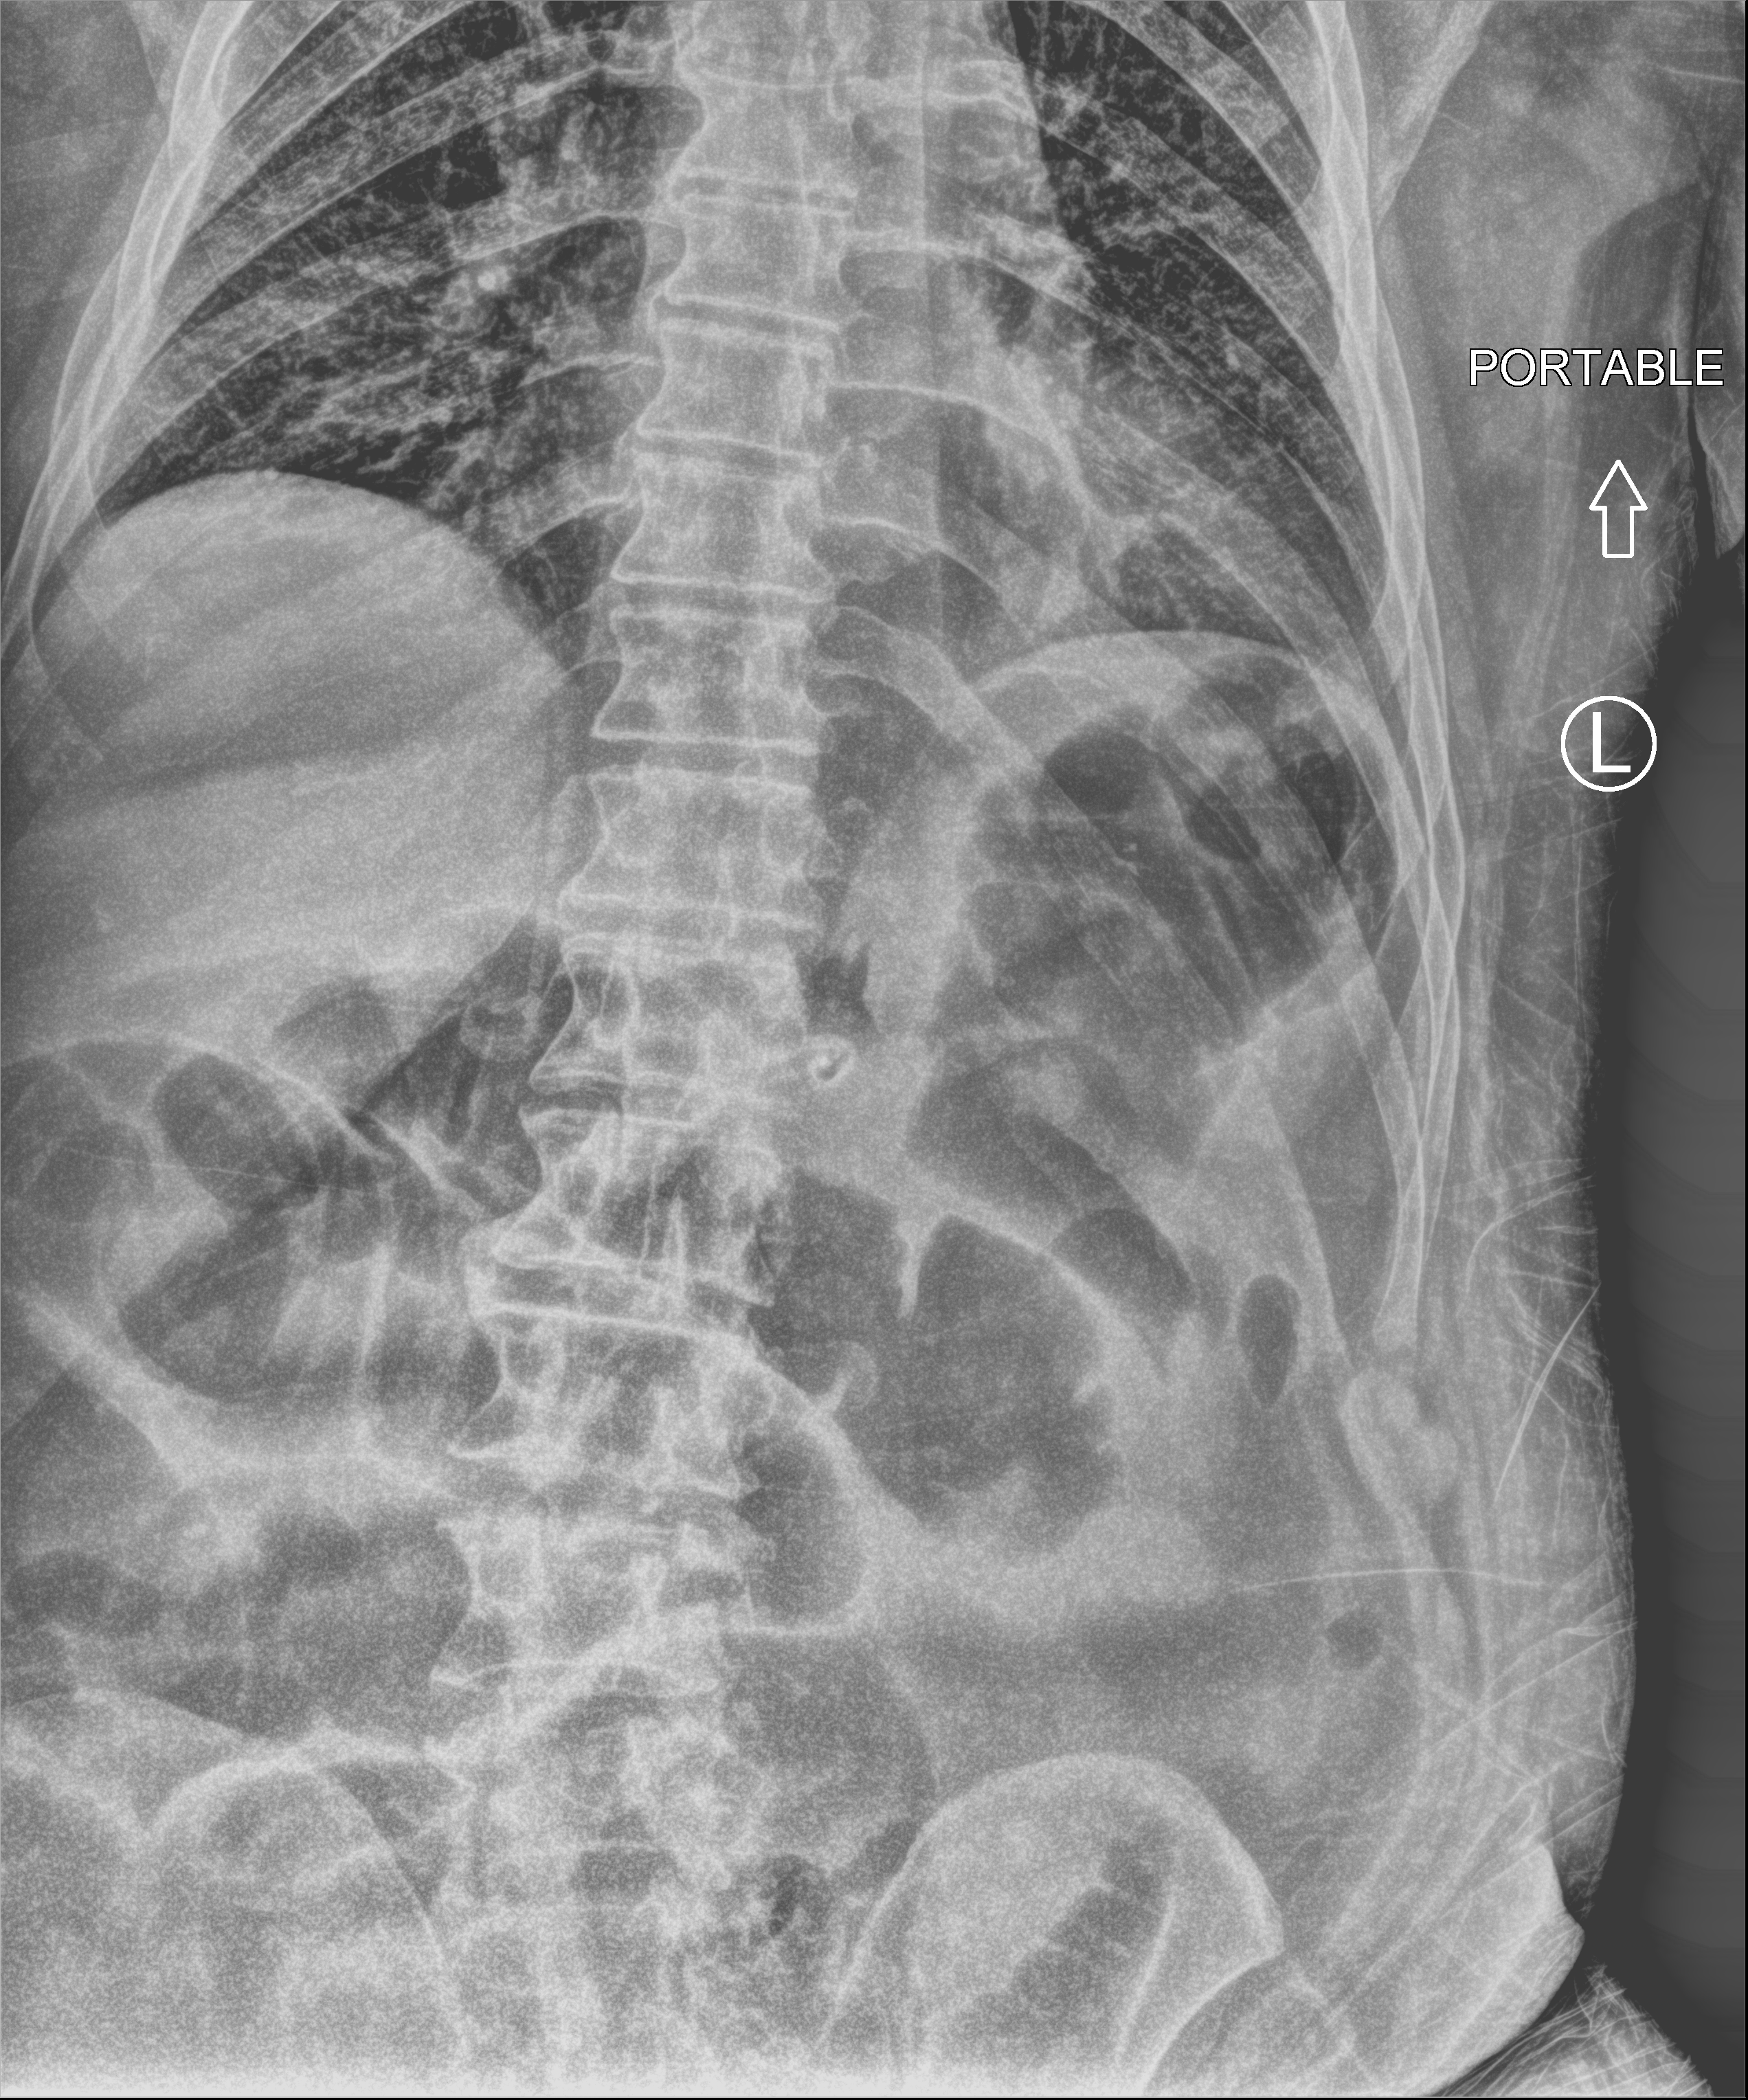
Portable abdomen radiograph, anteroposterior (AP) projection. Patient hospitalised with COVID-19; male, aged 60–74 years.
Hospital-stay facts (about this admission, not read from this image; timing relative to this image not recorded): hypertension (admission record): yes; admitted to intensive care during this hospital stay: no; mechanically ventilated during this hospital stay: no.